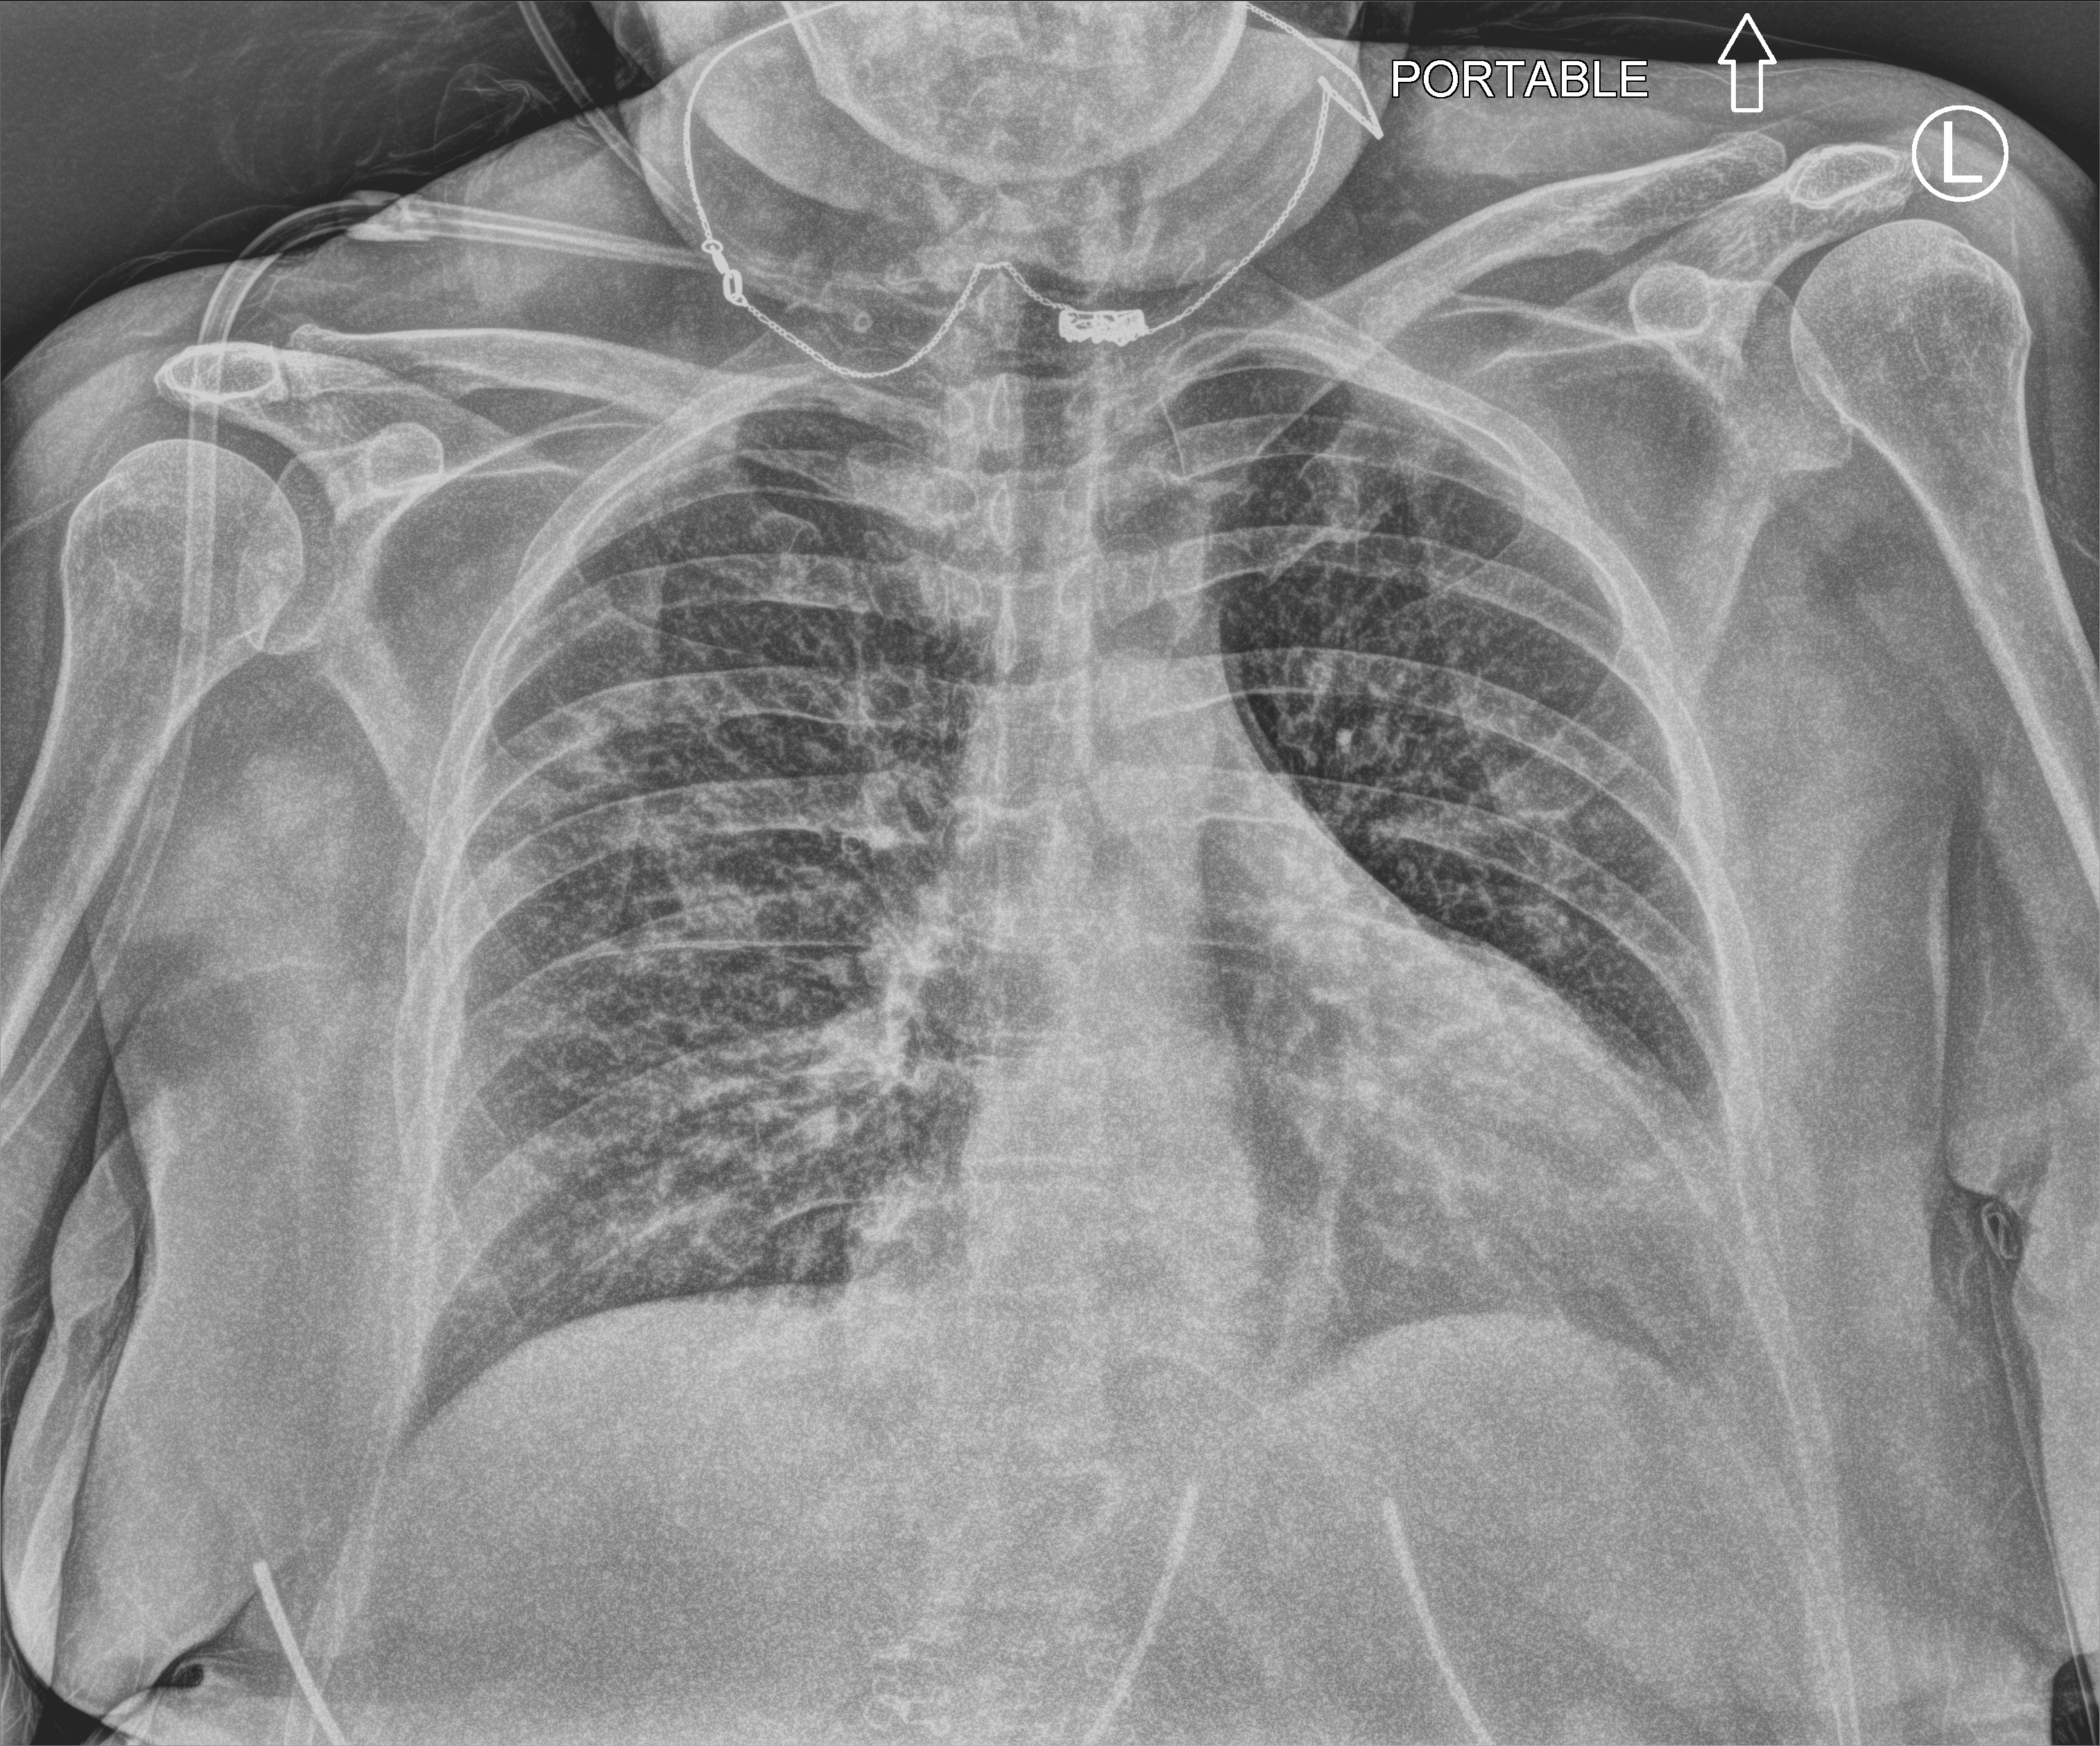
Portable chest radiograph; anteroposterior (AP) projection. Female patient hospitalised with COVID-19, age 18–59 years.
Hospital-stay facts (about this admission, not read from this image; timing relative to this image not recorded):
- mechanically ventilated during this hospital stay: no